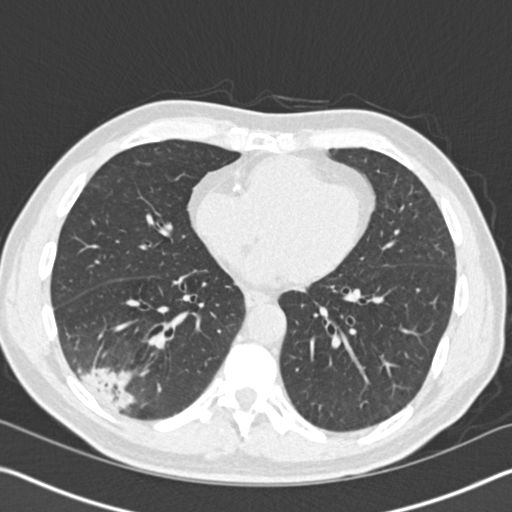
Low-dose screening chest CT, axial slice; baseline screening round; lung window (W 1500 / L -600 HU); 2 mm slice thickness; standard (soft-tissue) reconstruction kernel (B30f); slice 97 of 161 in the series. Male, age 61 years at enrolment. Current smoker at enrolment.
• Lesion marked by an expert reader, bounding box (x1, y1, x2, y2) in pixels: (45, 322, 156, 423).
• Screening reader's record for this exam (one nodule recorded; not confirmed to be the boxed lesion): non-calcified nodule or mass ≥4 mm, right lower lobe, 52 × 36 mm, spiculated (stellate) margins, soft tissue attenuation.
• Lung cancer was diagnosed 392 days after this screen (after the second annual screen): bronchiolo-alveolar adenocarcinoma, NOS, right lower lobe, moderately differentiated (G2), stage IIIB (AJCC 6th edition), 90 mm at pathology.